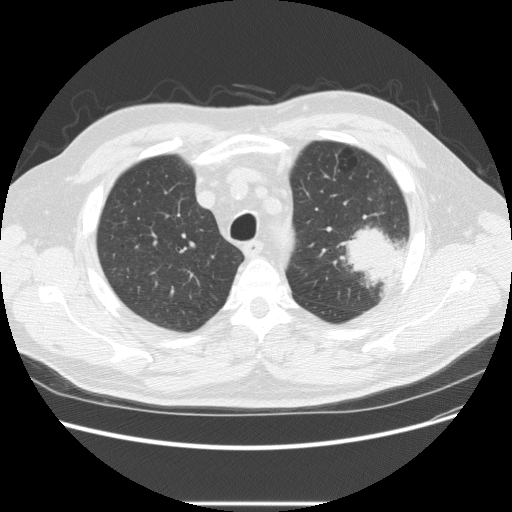
Low-dose screening chest CT, one axial slice. Slice 180 of 233 in the series (ordered by position). Reconstruction kernel STANDARD. 120 kVp. Lung window (W 1500 / L -600 HU). 2.5 mm slice thickness. 512 × 512 image matrix, field of view 380 × 380 mm.
Annotated regions visible in this slice (outlined manually by an expert reader):
- lesion 1 (tumor, upper lobe of left lung): bounding box (x1, y1, x2, y2) in pixels: (346, 226, 401, 294)